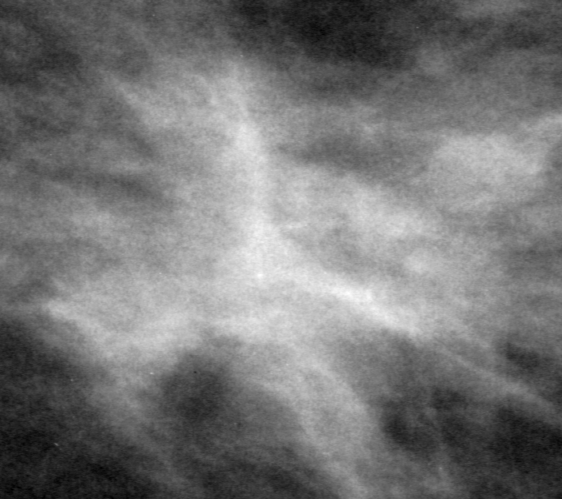
Crop from a digitized film mammogram around one marked abnormality; right breast; MLO view.
Mass, shape irregular, margins spiculated; BI-RADS assessment category 5; subtlety rating 5 on a 1 (subtle) to 5 (obvious) scale; pathology (as recorded): malignant.